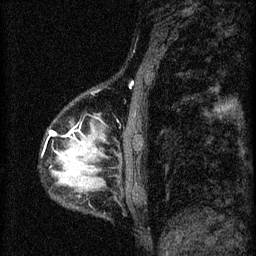
Breast MRI (dynamic contrast-enhanced), one sagittal slice; slice 11 of 60 in the series (ordered by position); 3 images stored at this slice position (order not interpretable as contrast timing); 1.5 T; TE 4.2 ms, TR 8.2 ms; 2 mm slice thickness; 256 × 256 image matrix, field of view 180 × 180 mm. Patient: female, 37 years.
Annotated regions visible in this slice (semi-automatically segmented with operator editing):
- analysis volume of interest (the breast-tissue region the enhancement analysis was run in; not a lesion): box from (x=44, y=114) to (x=119, y=197) px
- tumour enhancement mask (voxels above the 70 % enhancement threshold inside the analysis volume of interest): (x=53, y=132)–(x=83, y=143)